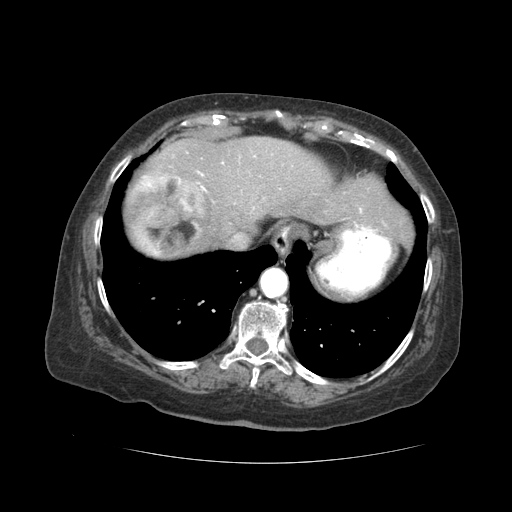
Contrast-enhanced abdominal CT (liver protocol), one axial slice; position 40 of 59 along the scan axis; reconstruction kernel STANDARD; 120 kVp; soft-tissue window (W 400 / L 40 HU); 2.5 mm slice thickness; 512 × 512 image matrix, field of view 380 × 380 mm. Case-level facts recorded for this patient, not image findings: diagnosis: hepatocellular carcinoma (patient treated with transarterial chemoembolisation; whether this scan precedes or follows treatment is not stated here); TNM stage (as recorded): Stage-I; Child-Pugh class: A; tumour nodularity: uninodular.
Annotated regions visible in this slice (semi-automatic segmentation, software-assisted and operator-edited):
- liver parenchyma outside the tumour (the mass and vessels are separate outlines, so this box may not span the whole liver): bounding box (x1, y1, x2, y2) in pixels: (128, 136, 412, 258)
- mass: (127, 174, 205, 254)
- liver vessels: (155, 163, 362, 254)